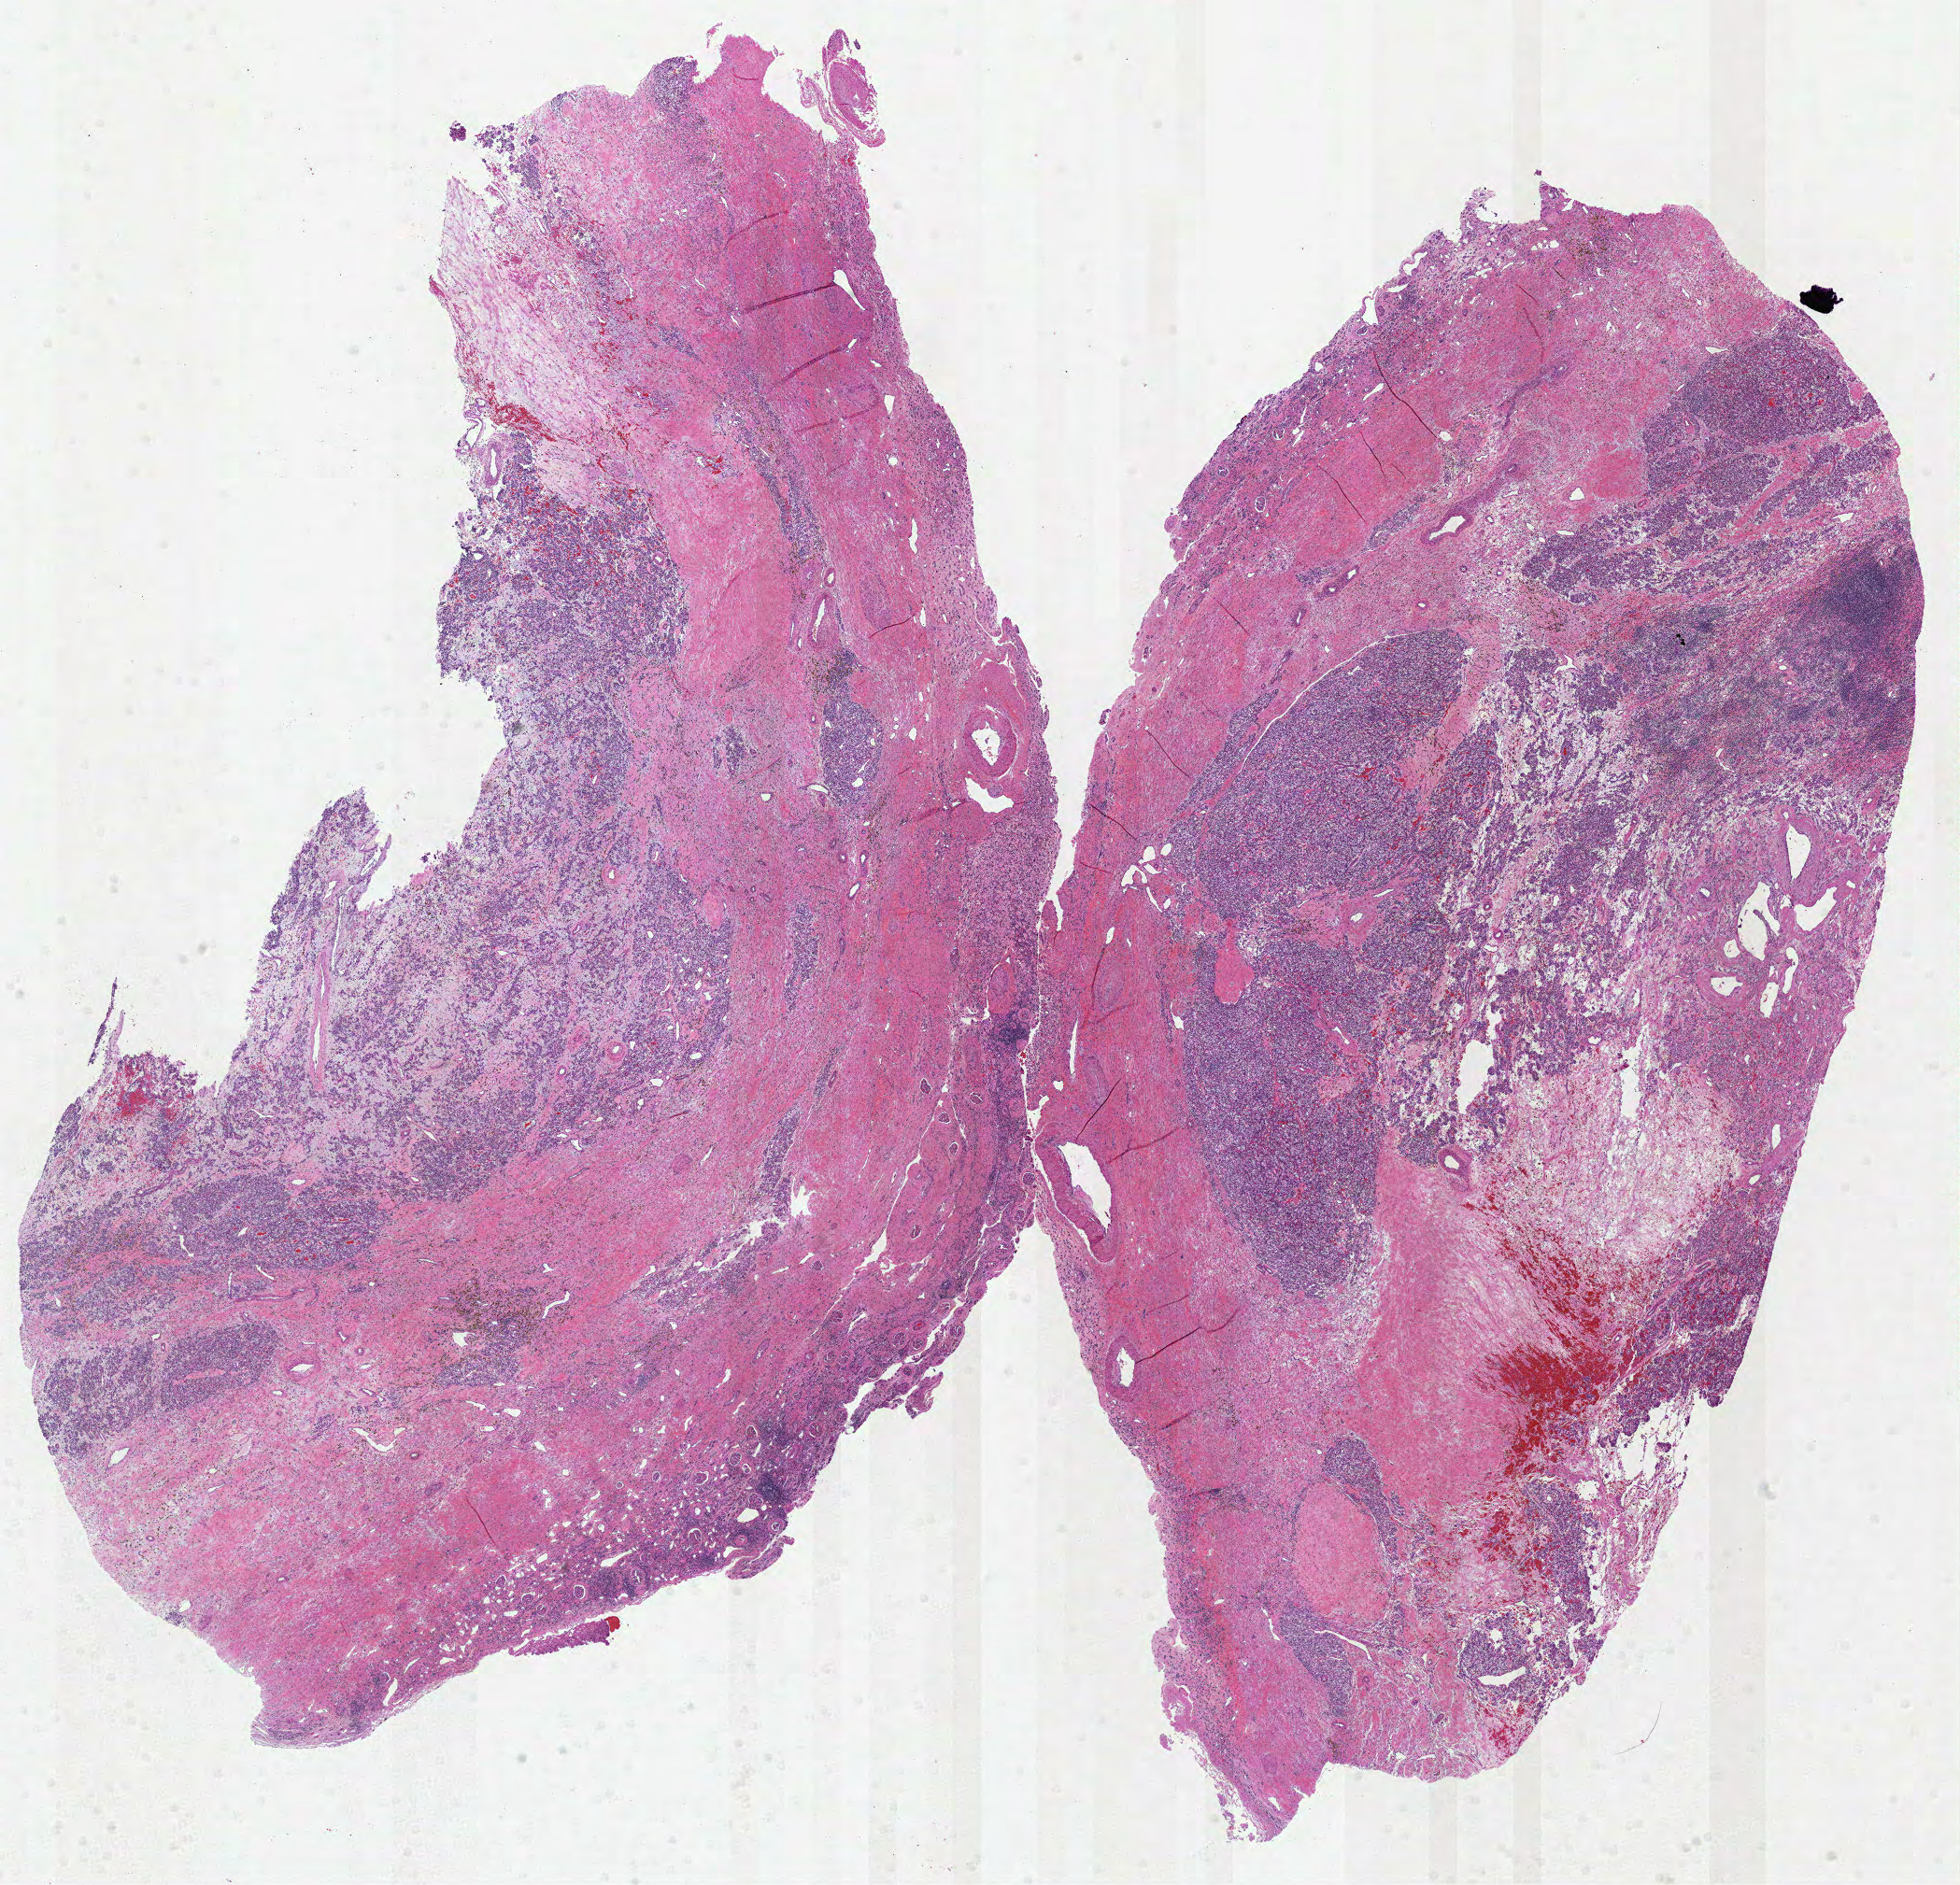
Digitized H&E tissue section (whole slide) — shown as a low-resolution overview of the whole scanned area (about 16.9 x 16.3 mm, acquisition: 40x scan); formalin-fixed paraffin-embedded (FFPE) diagnostic section; kidney, primary tumour sample. Male, age 37 years at initial diagnosis. Histologic grade: G2 (moderately differentiated).
Pathologic diagnosis: Clear cell adenocarcinoma, NOS. Laterality: right. AJCC pathologic stage: I.